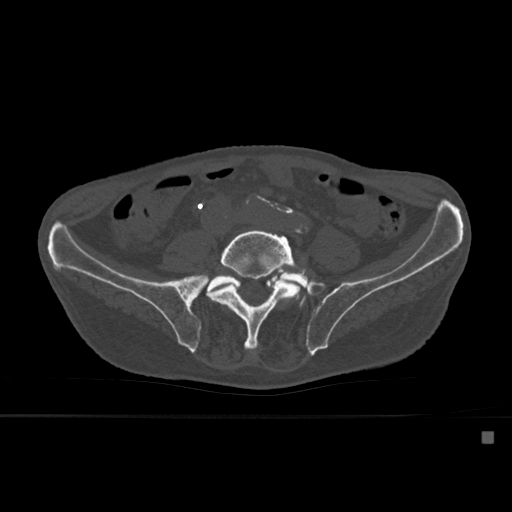
CT including the spine, one axial slice; slice 175 of 527 in the series (ordered by position); bone window (W 1800 / L 400 HU); 512 × 512 image matrix. Patient: male, 78 years. Case-level facts recorded for this patient, not image findings: primary cancer: prostate.
Structures marked on this image (semi-automatically segmented with operator editing):
- L4 vertebra: box from (x=225, y=298) to (x=289, y=308) px
- L5 vertebra: (x=207, y=229)–(x=314, y=350)